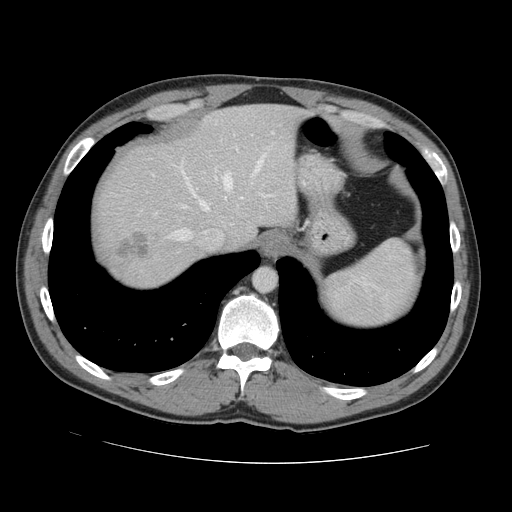
Contrast-enhanced abdominal CT, one axial slice. Slice 115 of 131 in the series (ordered by position). 120 kVp. Intravenous contrast given. Soft-tissue window (W 400 / L 40 HU). 512 × 512 image matrix, field of view 380 × 380 mm. Male patient, age 40 years. From the clinical record (not read from this slice): diagnosis: colorectal cancer liver metastases, imaged before liver resection; multiple liver metastases: yes; largest metastasis: 2.9 cm; chemotherapy before resection: yes.
Outlined on this slice (expert manual segmentation):
- hepatic veins: box from (x=174, y=155) to (x=264, y=241) px
- liver: (x=95, y=105)–(x=301, y=287)
- planned liver remnant (the part of the liver to remain after resection): (x=112, y=105)–(x=301, y=247)
- portal vein (with intrahepatic branches): (x=215, y=176)–(x=264, y=196)
- liver metastasis: (x=115, y=232)–(x=152, y=259)